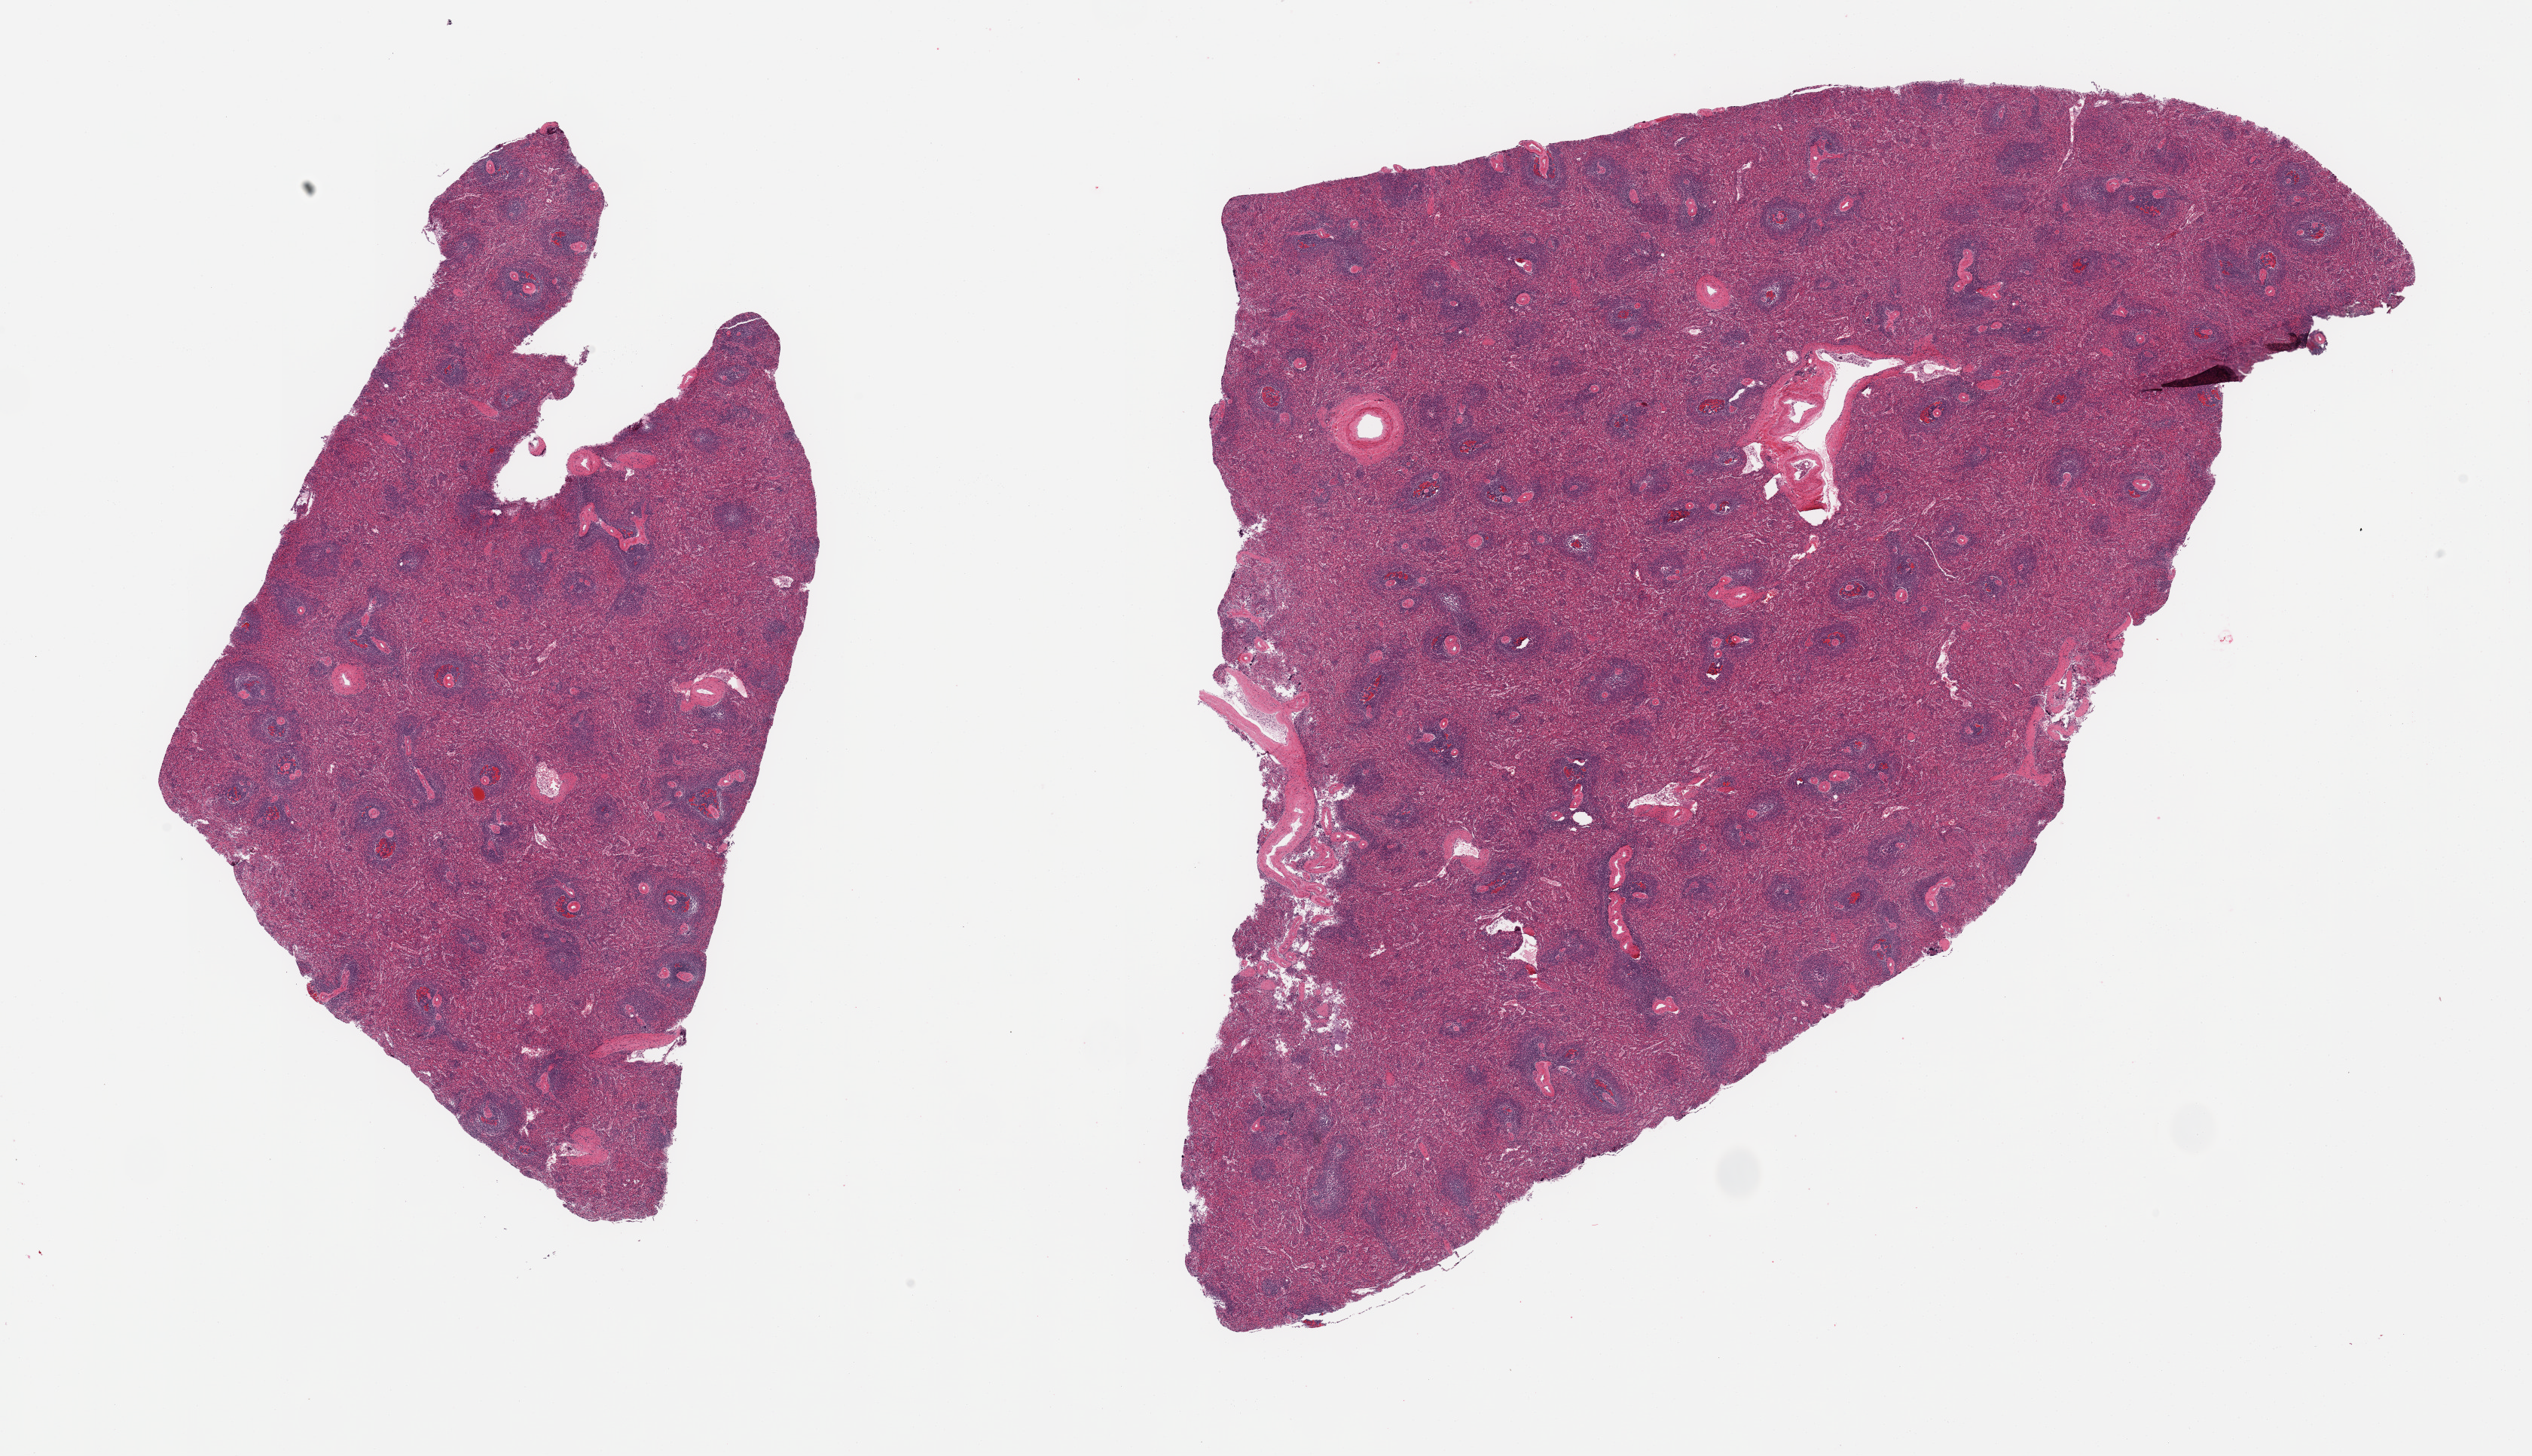
Hematoxylin and eosin (H&E) whole-slide image — low-resolution overview of the scanned area, about 26.6 x 15.3 mm (from a 20x scan), PAXgene-fixed paraffin-embedded (PFPE) section, section of spleen (target tissue), donor tissue sample. Female donor.
* review note (as recorded): 2 pieces